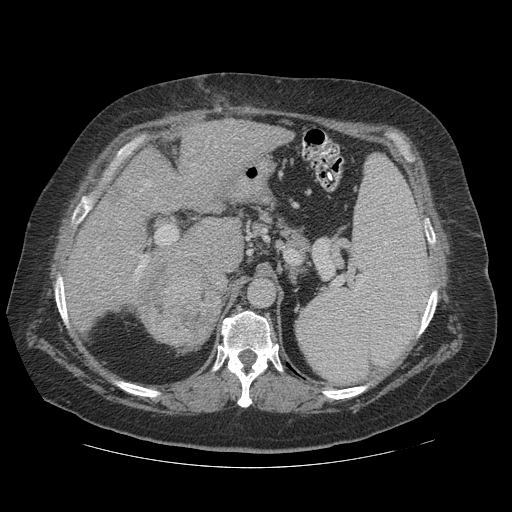
Contrast-enhanced abdominal CT (liver protocol), one axial slice. Slice 74 of 121 in the series (ordered by position). Reconstruction kernel STANDARD. Soft-tissue window (W 400 / L 40 HU). 512 × 512 image matrix, field of view 420 × 420 mm. From the clinical record (not read from this slice): diagnosis: hepatocellular carcinoma (patient treated with transarterial chemoembolisation; whether this scan precedes or follows treatment is not stated here); TNM stage (as recorded): Stage-IIIA; Child-Pugh class: A; tumour differentiation: well differentiated; tumour nodularity: multinodular.
Outlined on this slice (semi-automatic segmentation, software-assisted and operator-edited):
- liver parenchyma outside the tumour (the mass and vessels are separate outlines, so this box may not span the whole liver): box from (x=66, y=120) to (x=294, y=320) px
- mass: (x=135, y=257)–(x=221, y=351)
- liver vessels: (x=94, y=129)–(x=244, y=293)